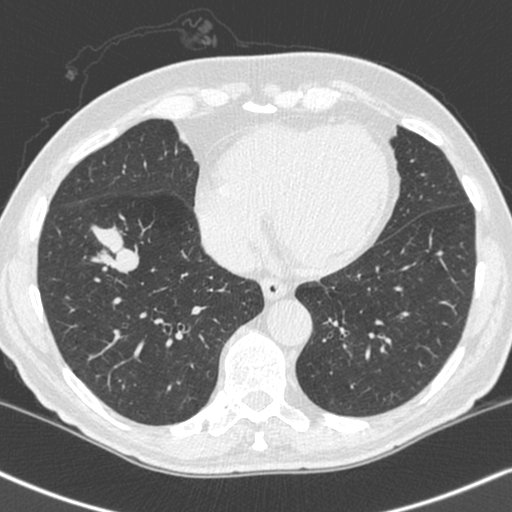
Axial slice from a low-dose chest CT screening exam, baseline screening round, lung window (W 1500 / L -600 HU), 1.3 mm slice thickness, slice 157 of 248 in the series, 512 × 512 image matrix, field of view 323 × 323 mm. Male, age 68 years at enrolment.
Expert-annotated lung lesion, bounding box <79,206,154,275> (left, top, right, bottom; pixels). Reader record for this screening exam (exam-level; its link to the box is not recorded): non-calcified nodule or mass ≥4 mm, right lower lobe, 34 × 17 mm, smooth margins, soft tissue attenuation.